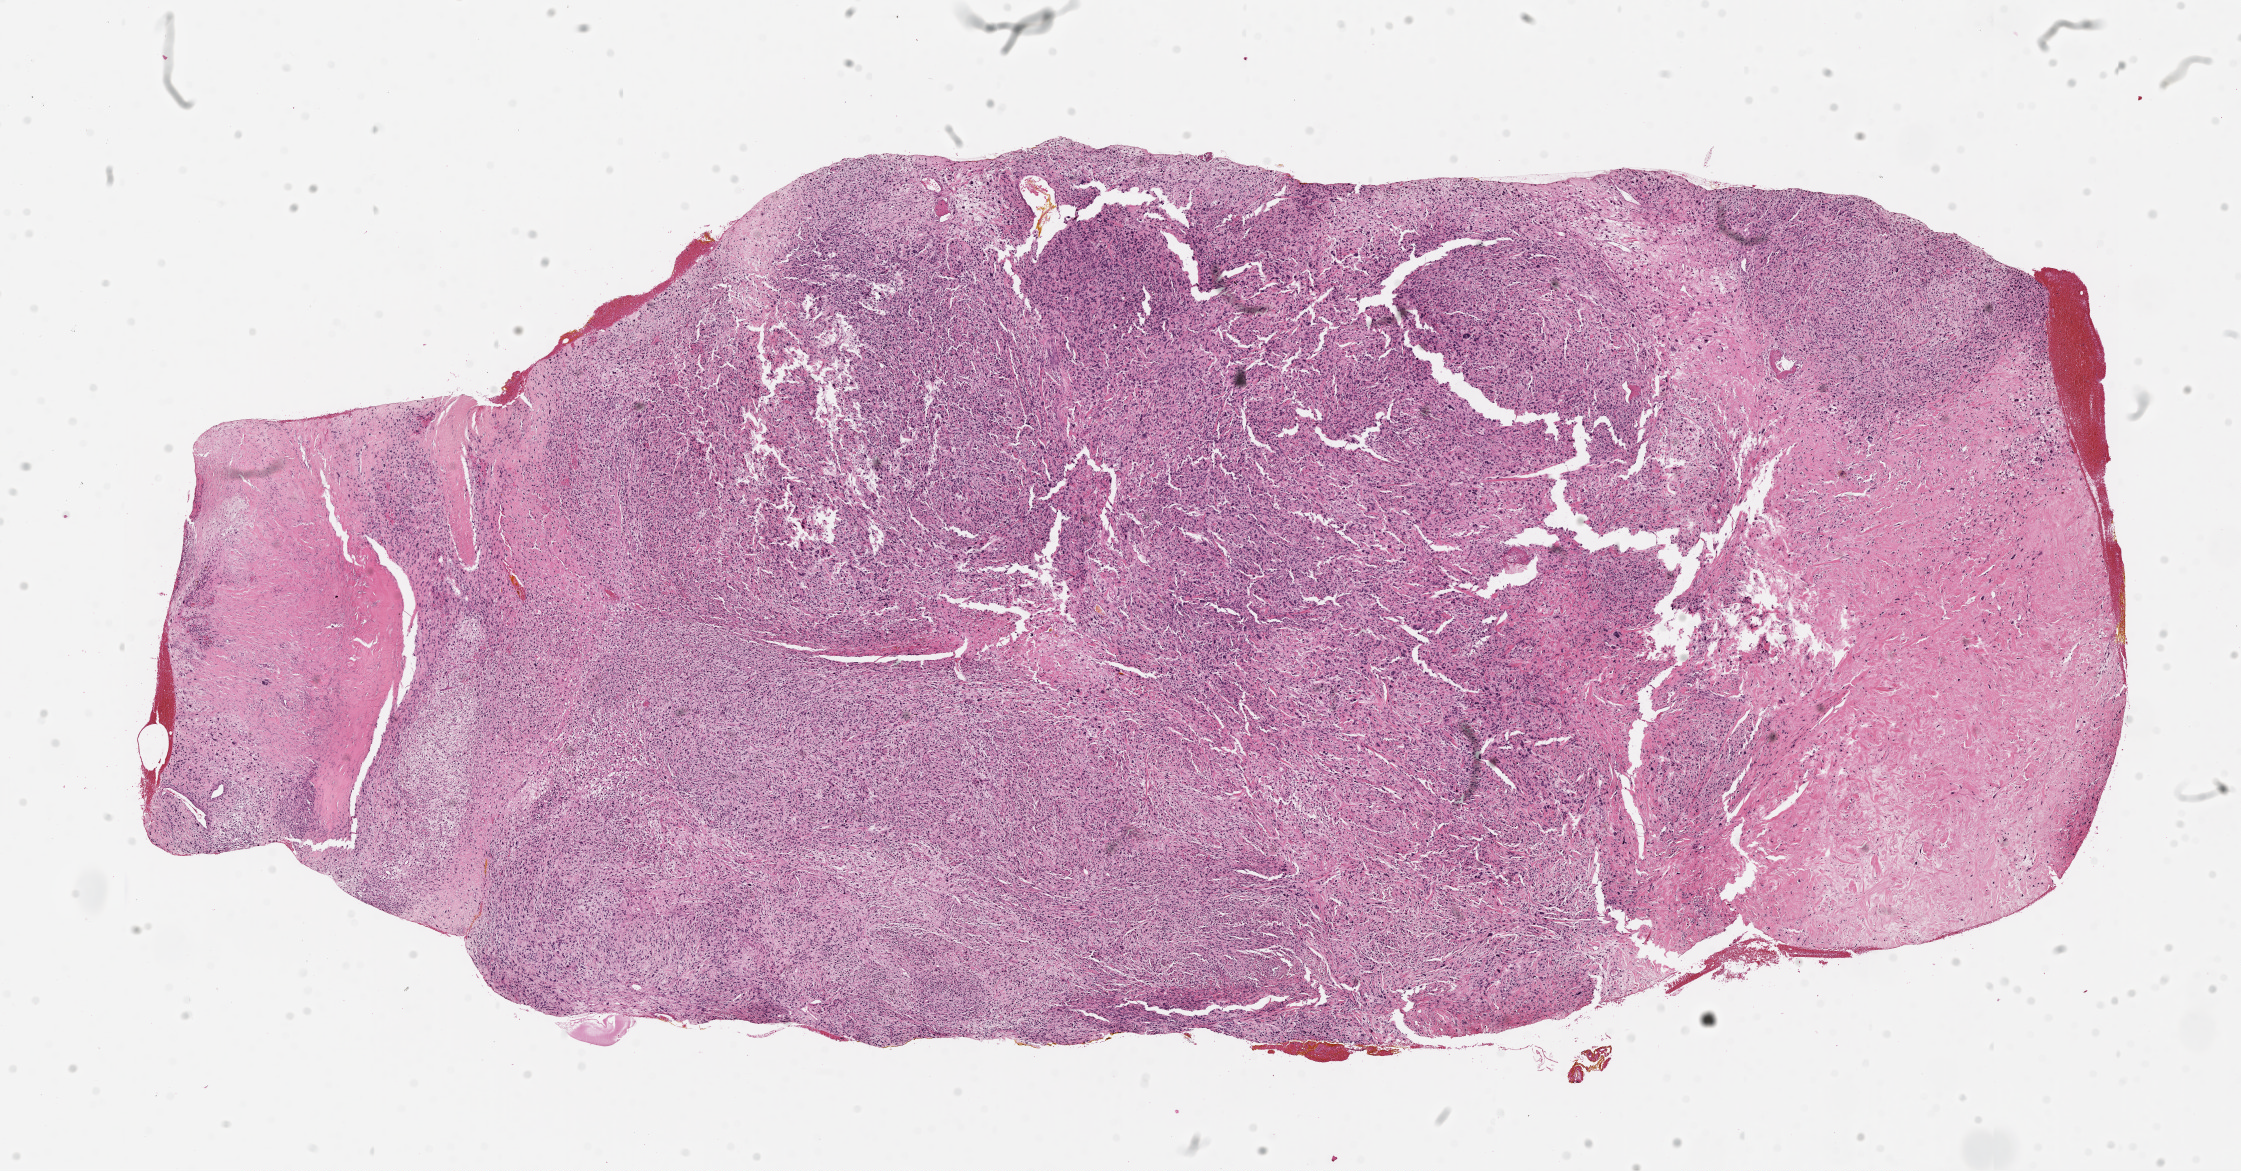
H&E-stained whole-slide image, whole scanned area (about 18.0 x 9.4 mm, acquisition: 20x scan) shown as a low-resolution overview.
• patient diagnosis (cohort enrolment): sarcoma (site not recorded at cohort level)